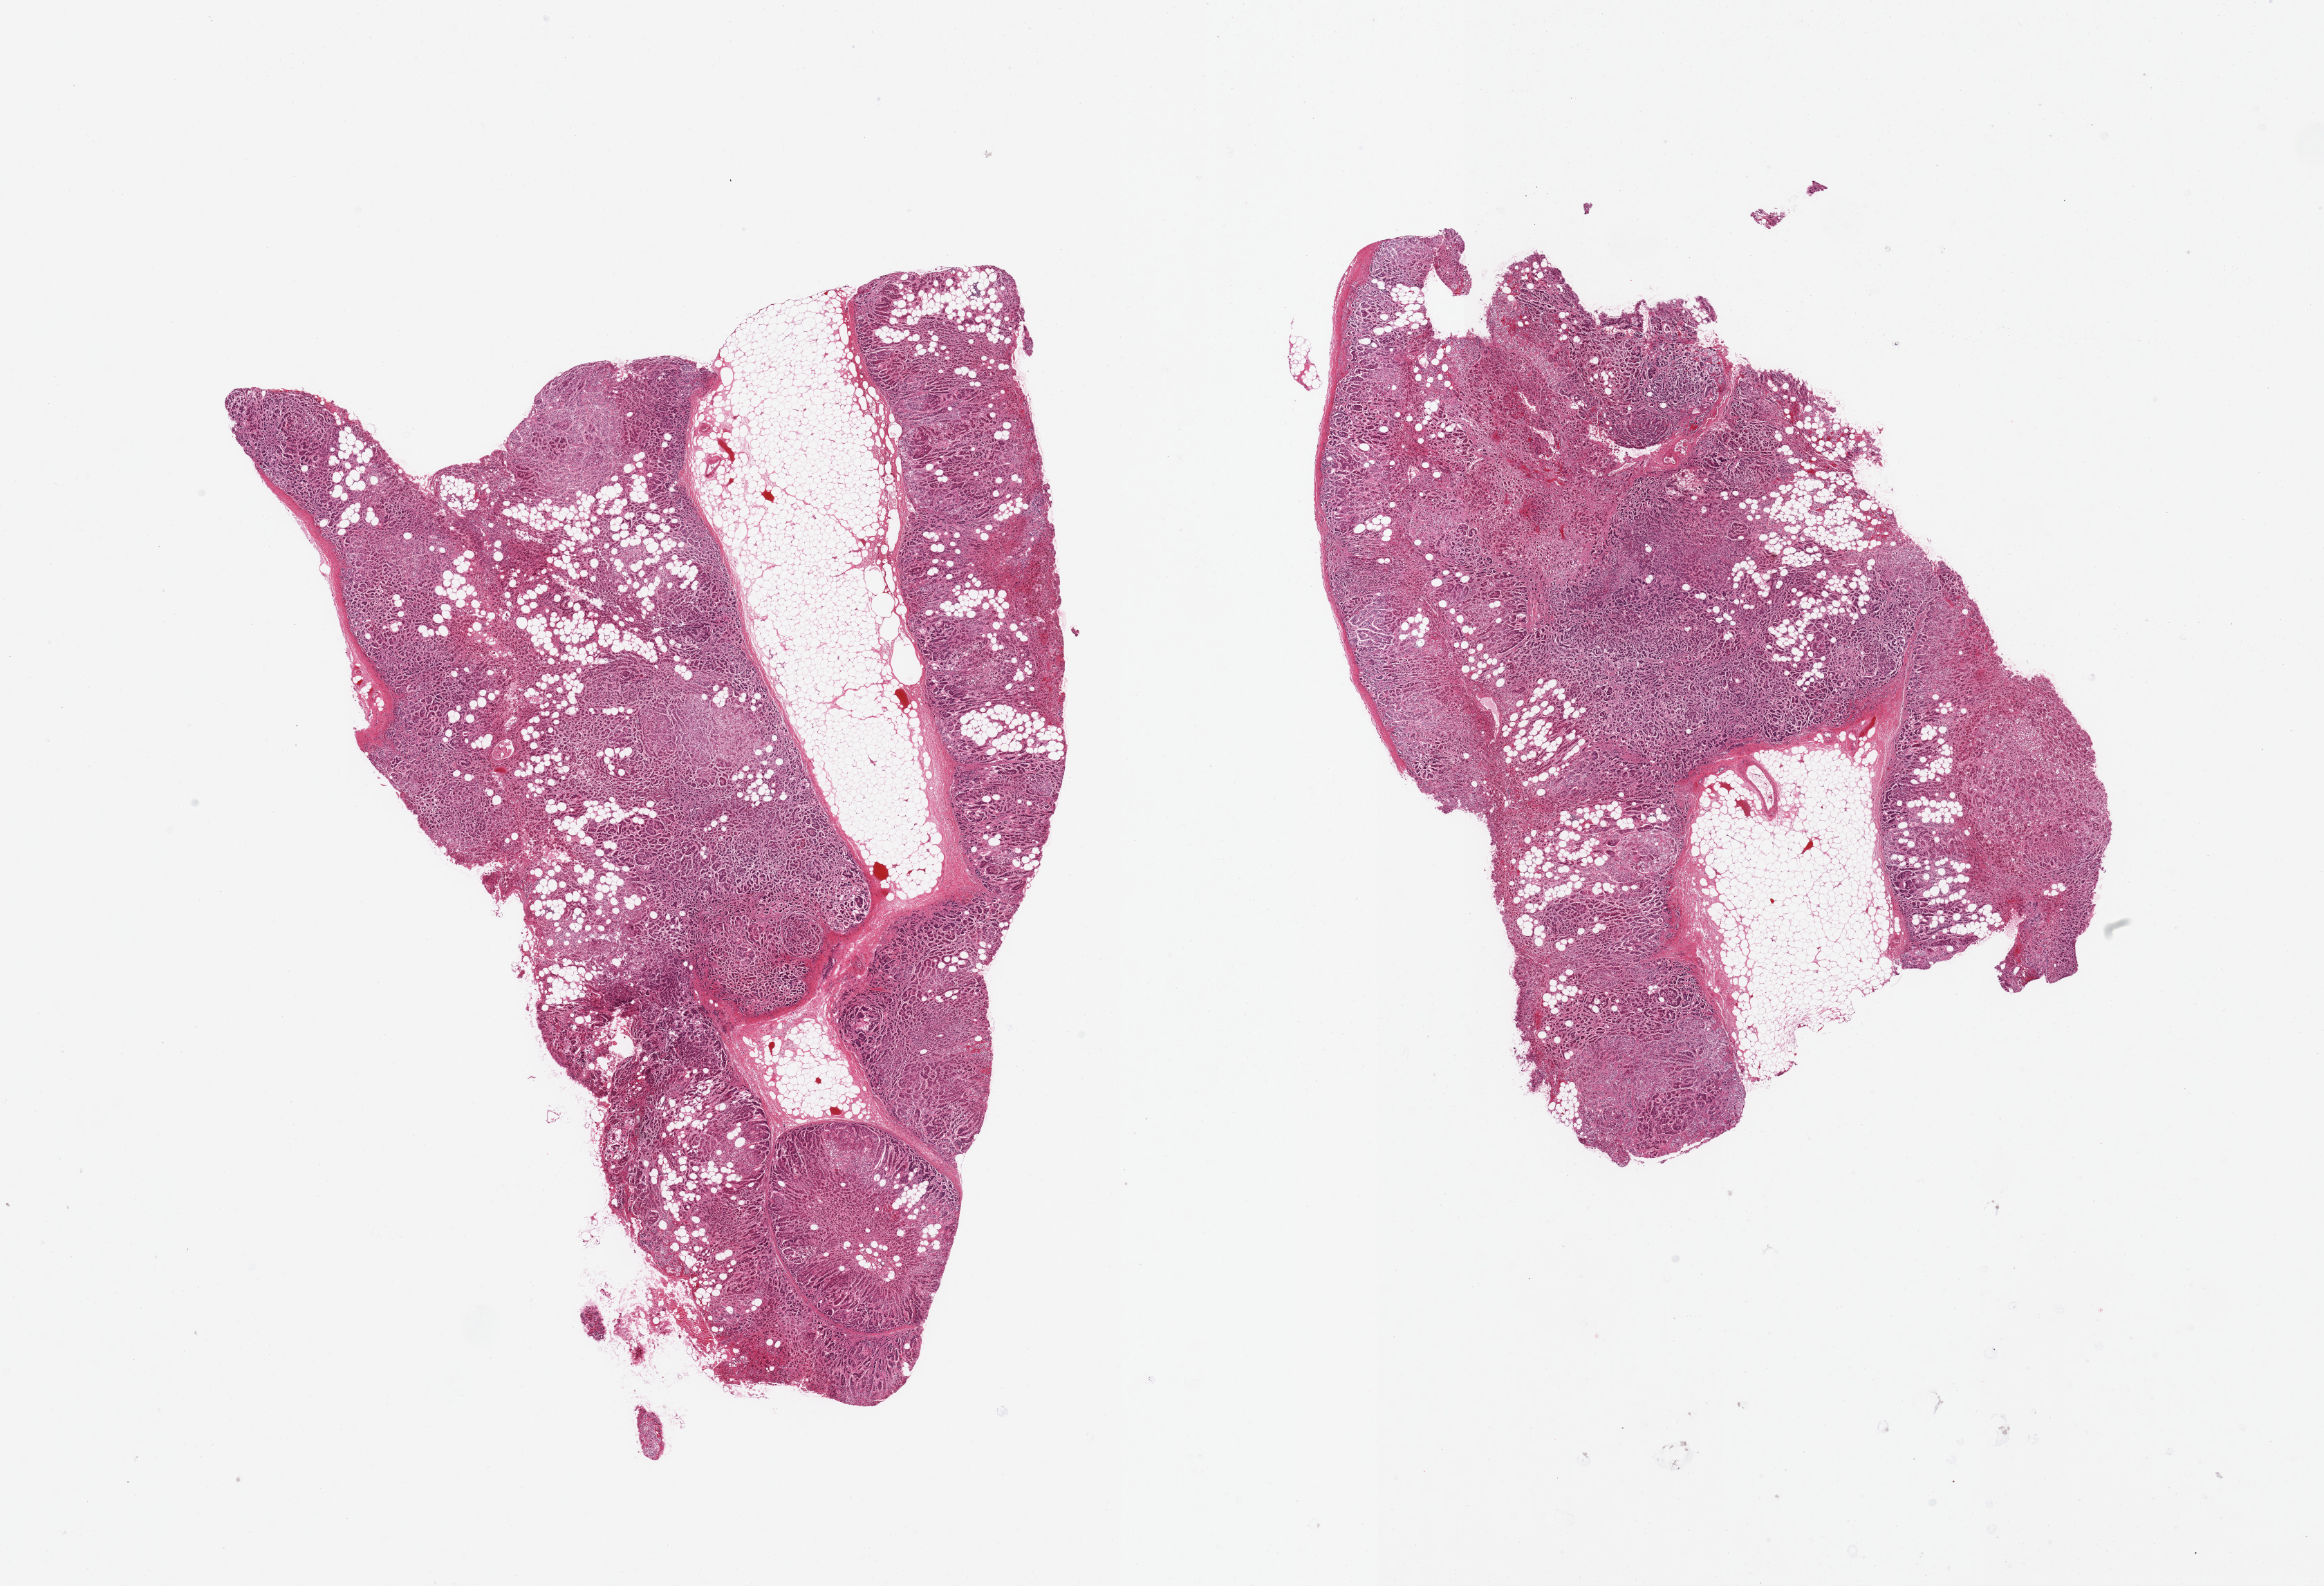
Digitized hematoxylin and eosin (H&E)-stained section — a low-resolution overview of the entire scanned area, about 26.6 x 18.1 mm; PAXgene-fixed paraffin-embedded (PFPE) section; target tissue: adrenal gland; donor tissue sample. Male donor.
Pathologist's review note for this sample: 2 pieces; moderate to severe autolysis of adrenal cortex; ~25-30% internal/ external fat; congestion.